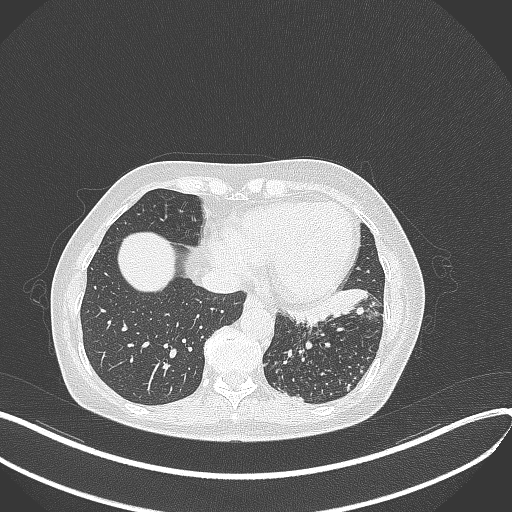
Chest CT, one axial slice; slice 119 of 429 in the series (ordered by position); reconstruction kernel B70f; lung window (W 1500 / L -600 HU); 1 mm slice thickness; 512 × 512 image matrix, field of view 400 × 400 mm. Patient: female, 63 years. Case-level facts recorded for this patient, not image findings: clinical TNM (as recorded): T1b N0 M0; histopathological grade: G2-3.
Annotated regions visible in this slice (bounding box drawn by a radiologist):
- lung tumour (recorded histology: adenocarcinoma): bounding box [x1, y1, x2, y2] px = [282, 284, 372, 329]